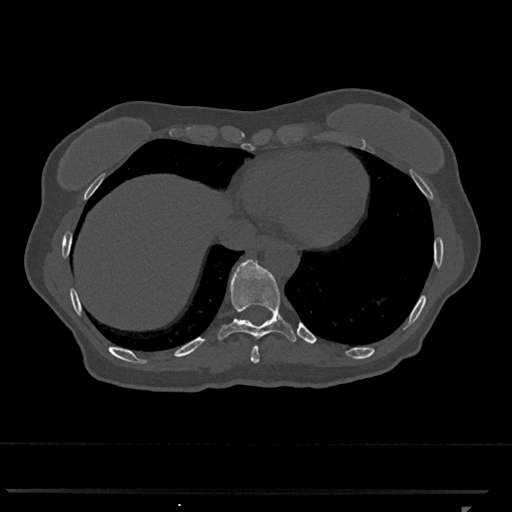
CT including the spine, one axial slice; position 572 of 793 along the scan axis; 120 kVp; bone window (W 1800 / L 400 HU); 0.5 mm slice thickness; 512 × 512 image matrix, field of view 380 × 380 mm. Female patient, age 62 years. Case-level facts recorded for this patient, not image findings: primary cancer: renal.
Annotated regions visible in this slice (semi-automatically segmented with operator editing):
- T10 vertebra: bounding box [x1, y1, x2, y2] px = [218, 260, 297, 342]
- T9 vertebra: [251, 346, 259, 363]